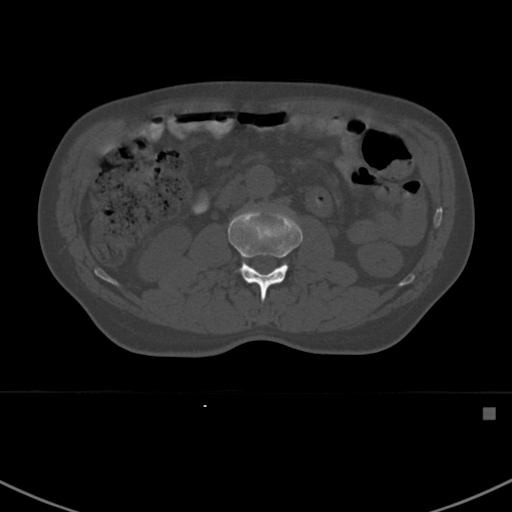
CT including the spine, one axial slice. Position 284 of 412 along the scan axis. Reconstruction kernel Br40s. Bone window (W 1800 / L 400 HU). 1.5 mm slice thickness. 512 × 512 image matrix. Male patient, age 59 years. From the clinical record (not read from this slice): primary cancer: prostate.
Outlined on this slice (semi-automatically segmented with operator editing):
- L2 vertebra: box from (x=228, y=207) to (x=303, y=302) px